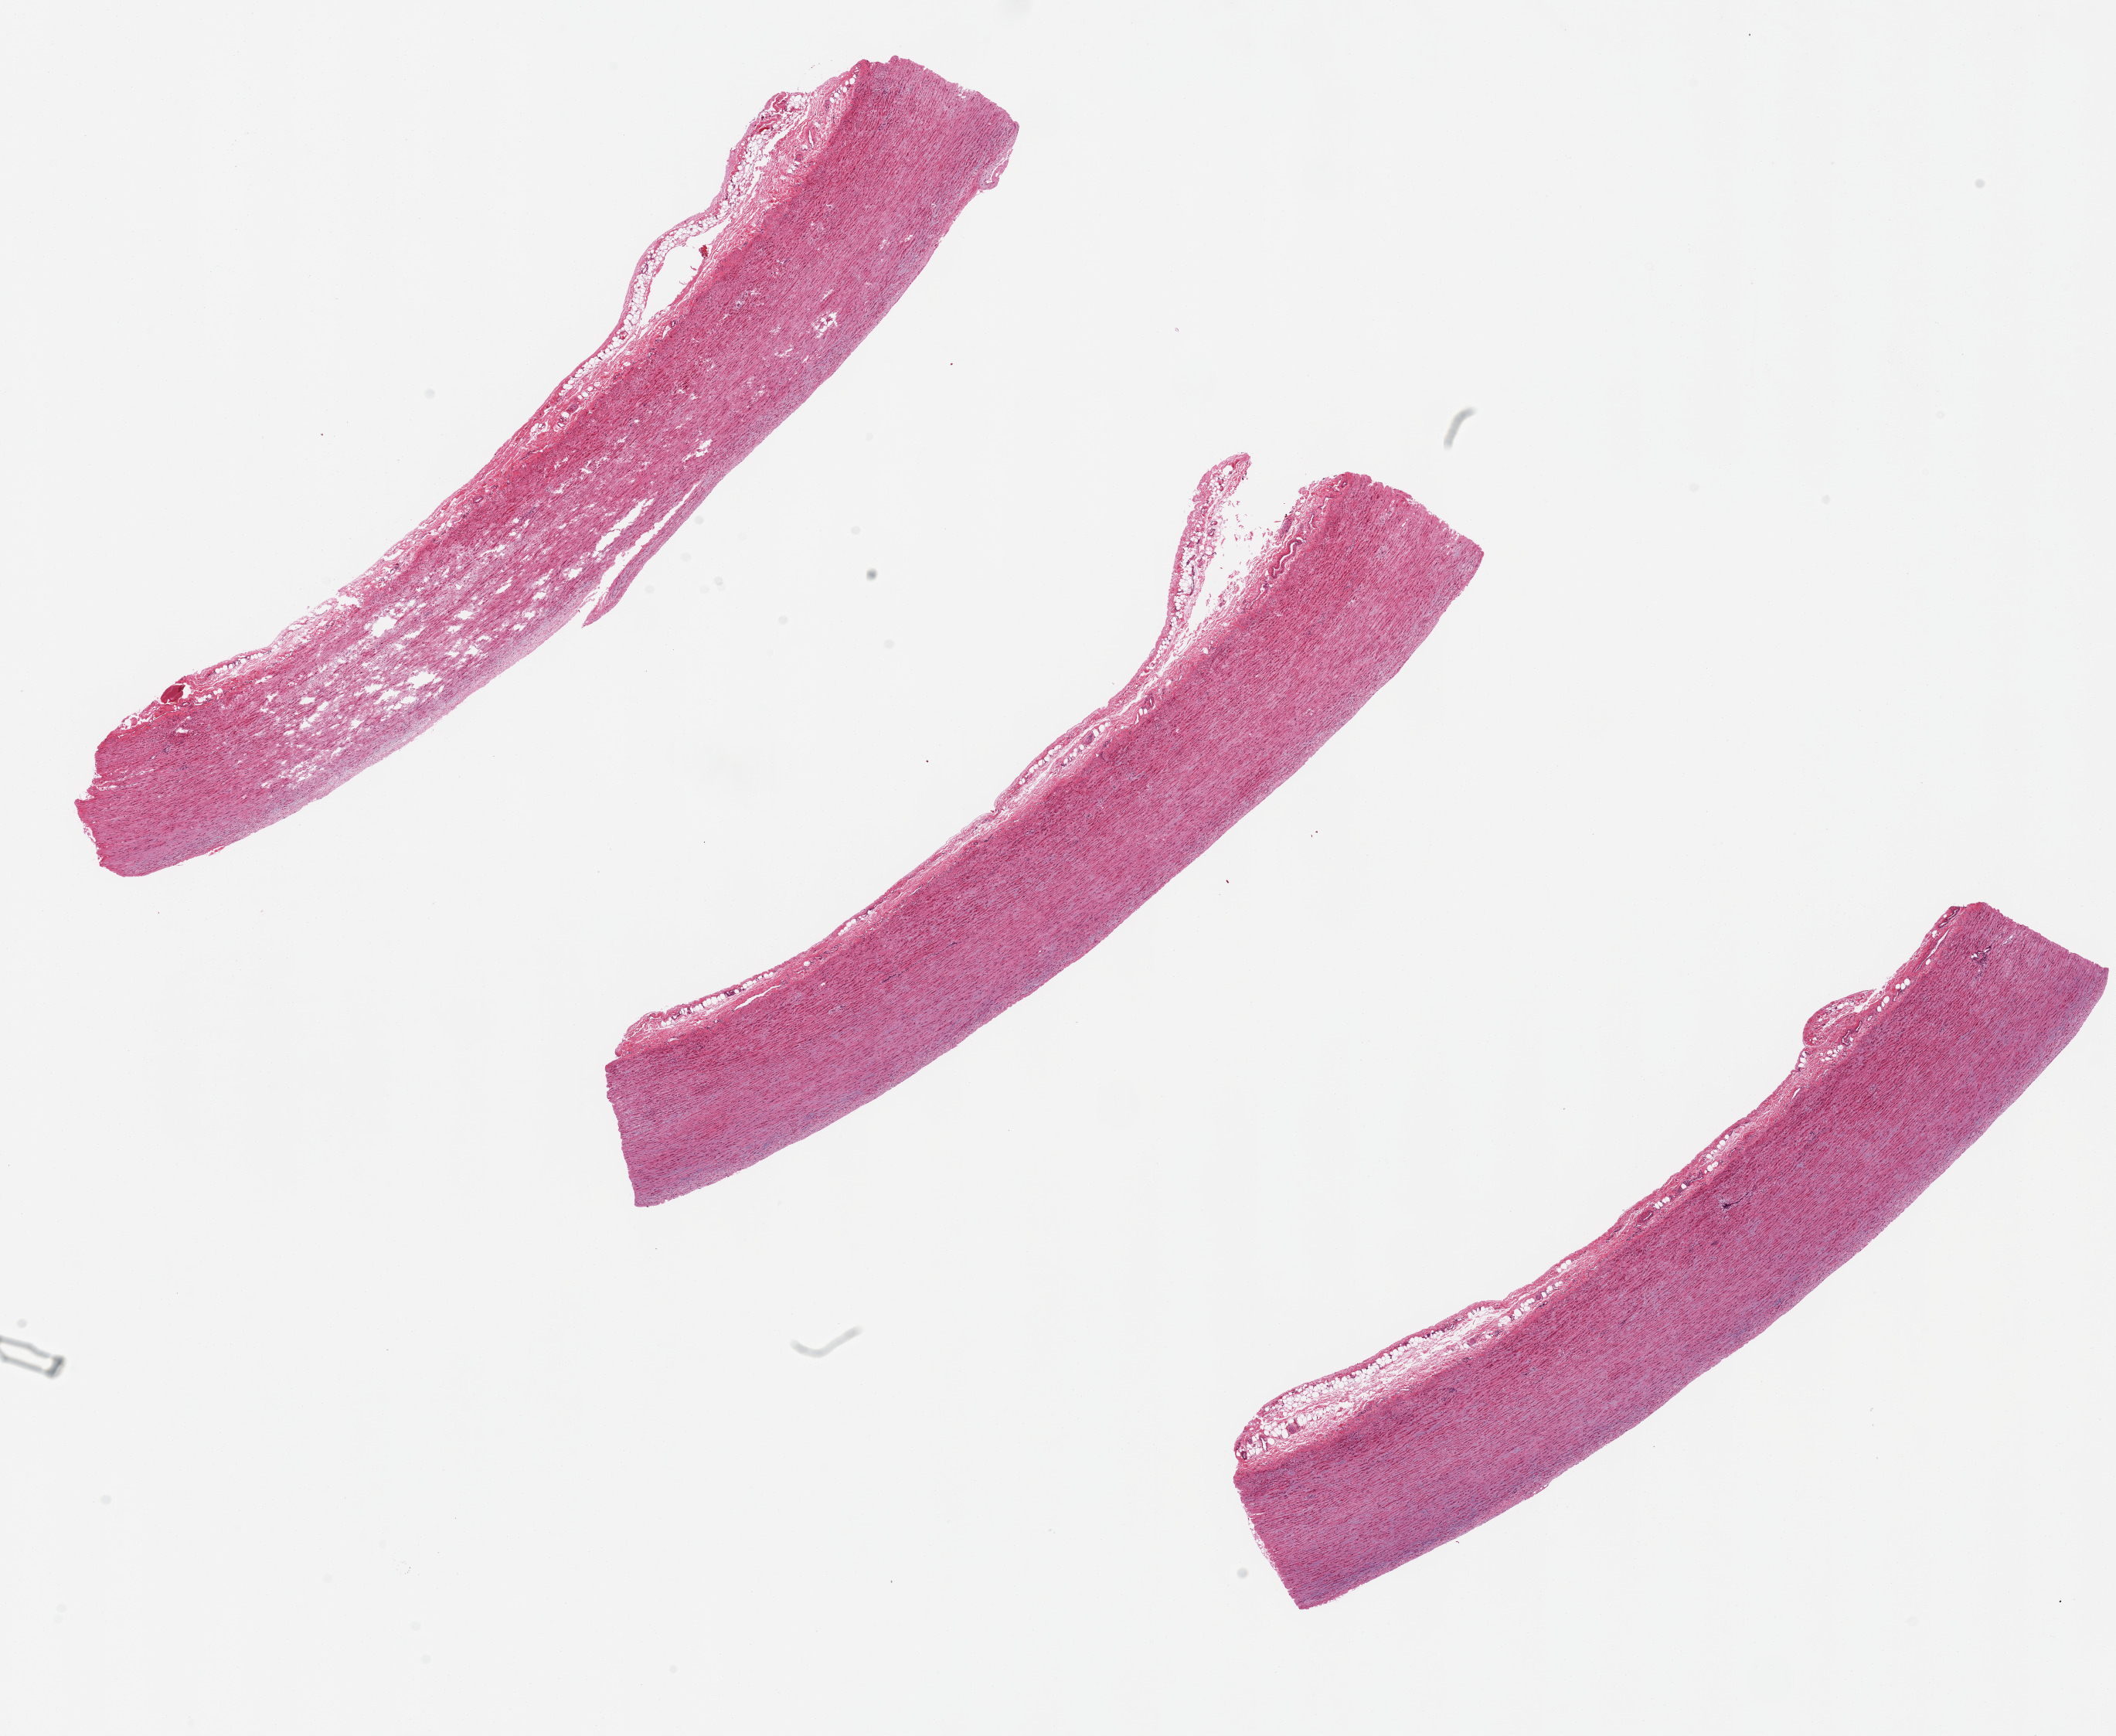
Digitized H&E-stained section — shown as a low-resolution overview of the whole scanned area (about 21.7 x 17.8 mm); PAXgene-fixed, paraffin-embedded tissue; target tissue: aorta; donor tissue sample. Male donor.
Pathologist's review note for this sample: 3 pieces: 11x1.8 mm.